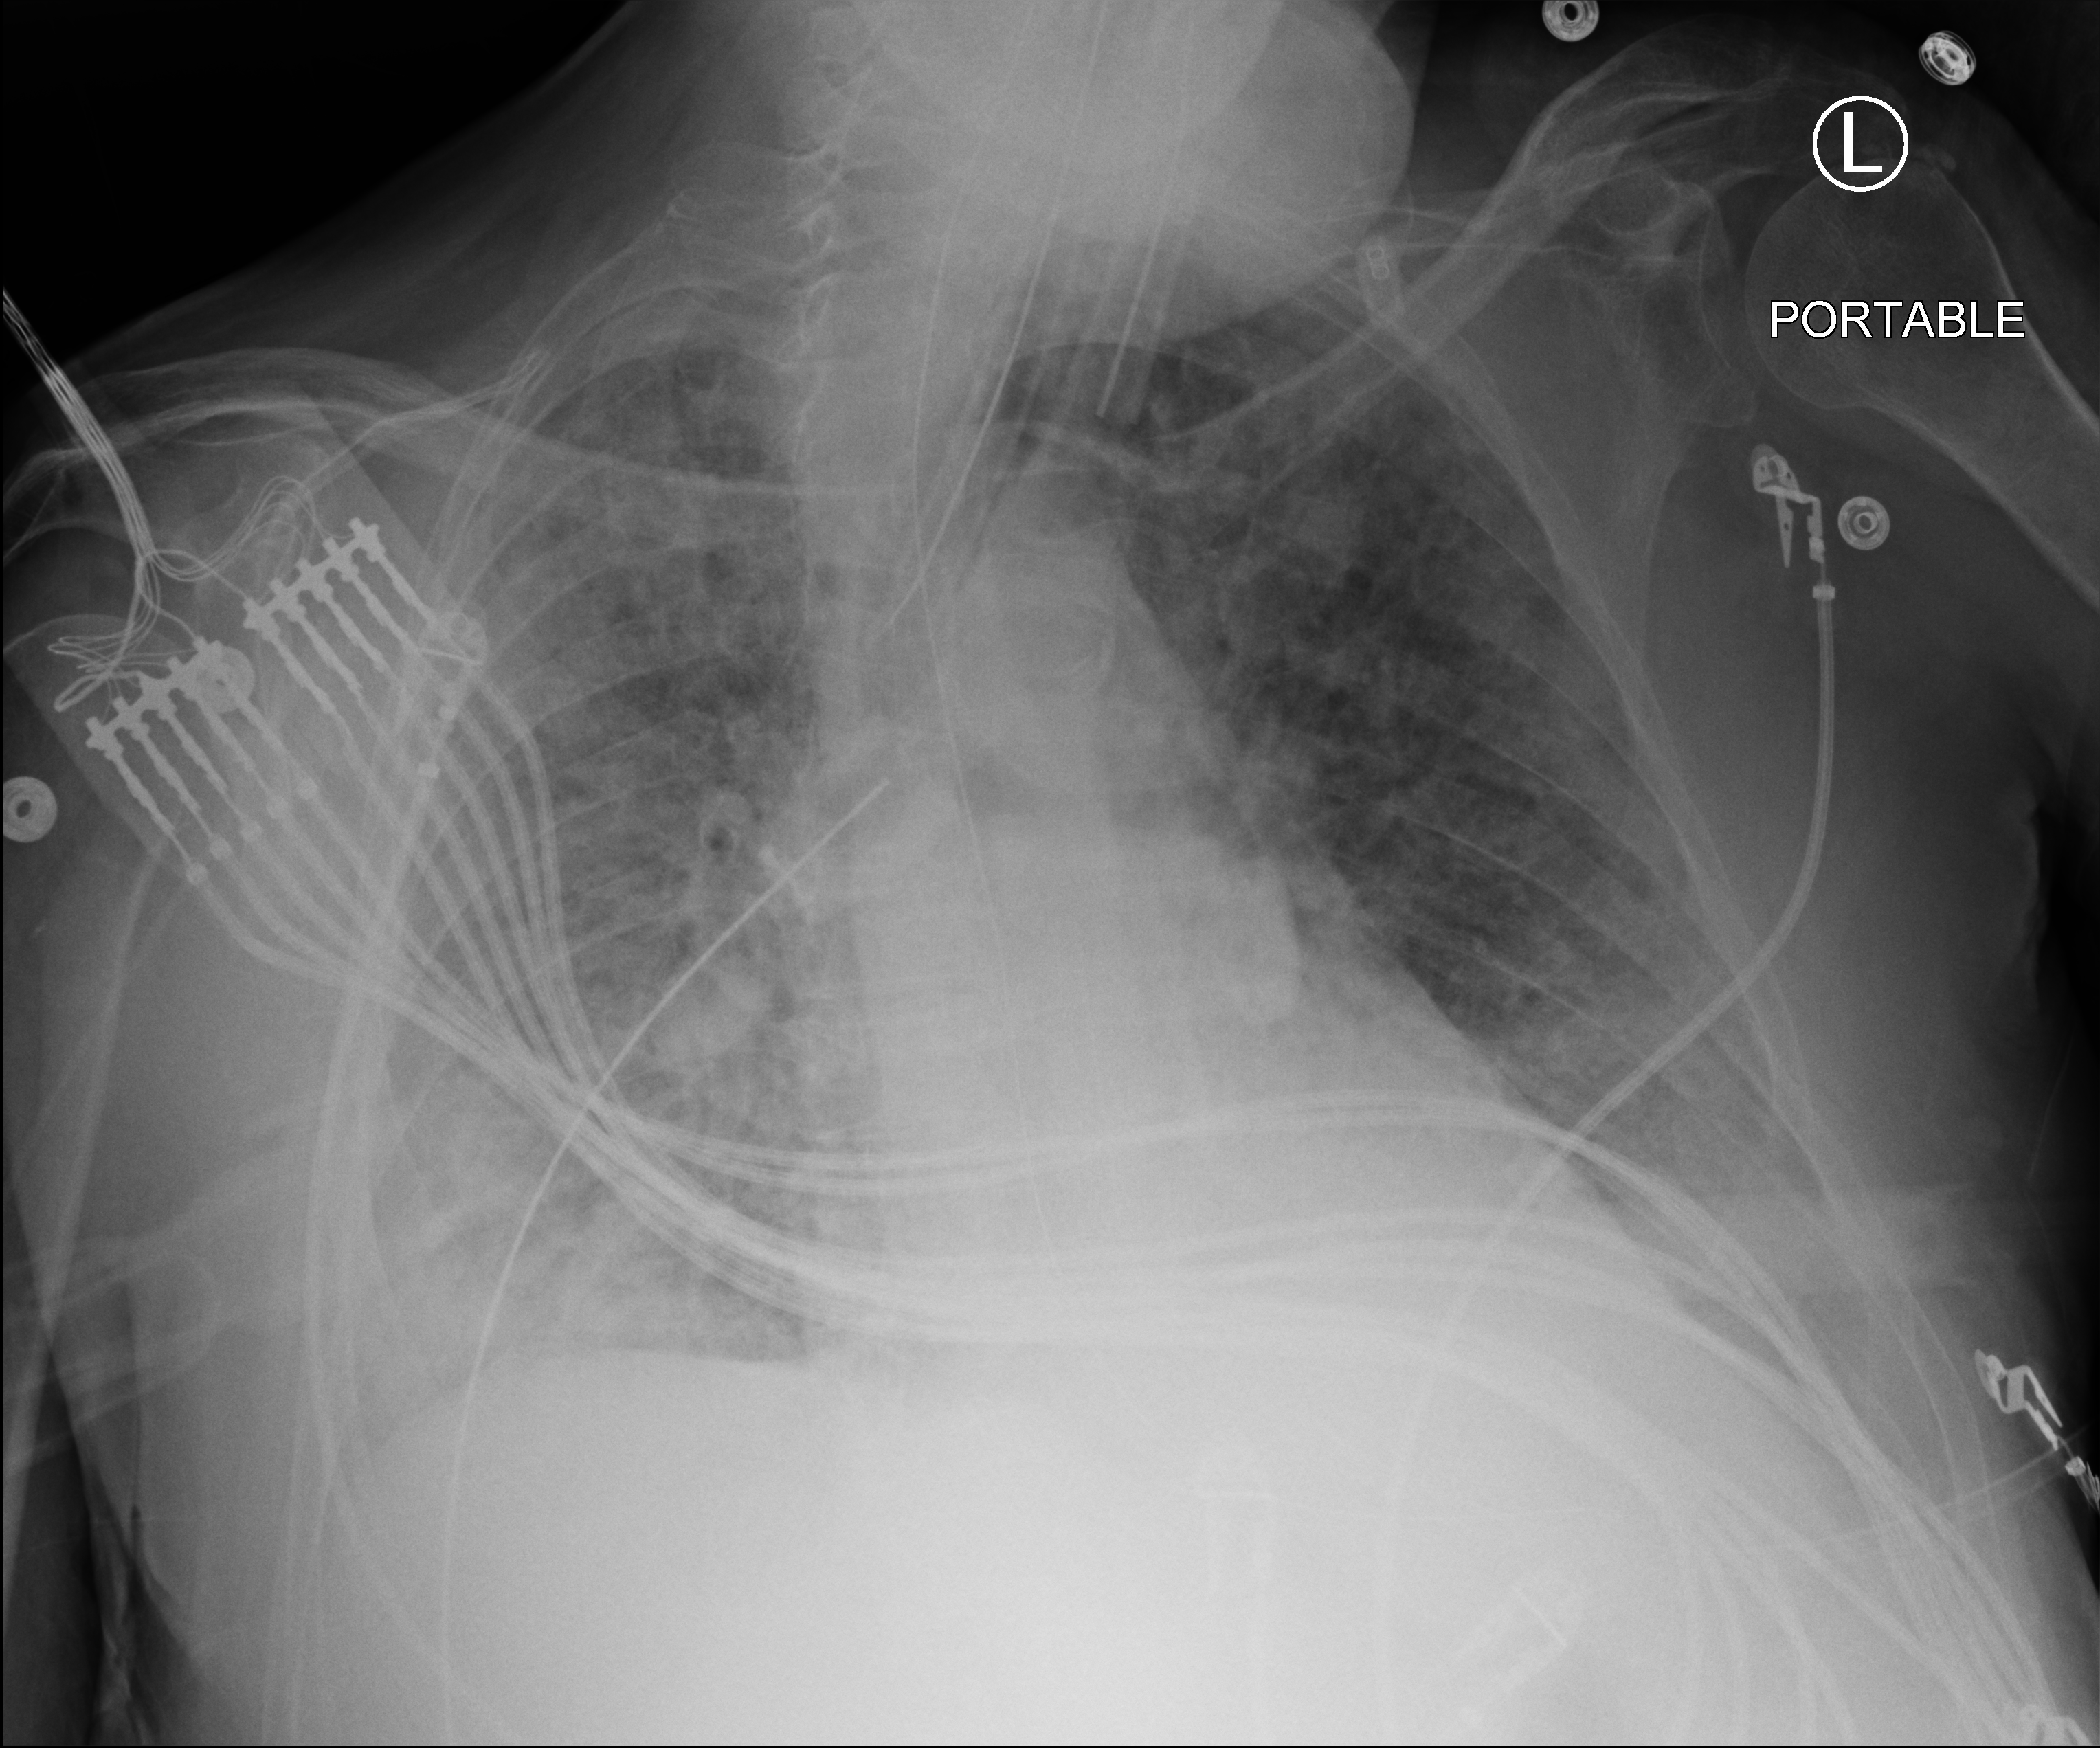
Chest X-ray (portable). Patient hospitalised with COVID-19; male, aged 60–74 years.
Admission-level facts for this patient (not findings on this image; timing relative to this image not recorded):
- smoking status (admission record): never